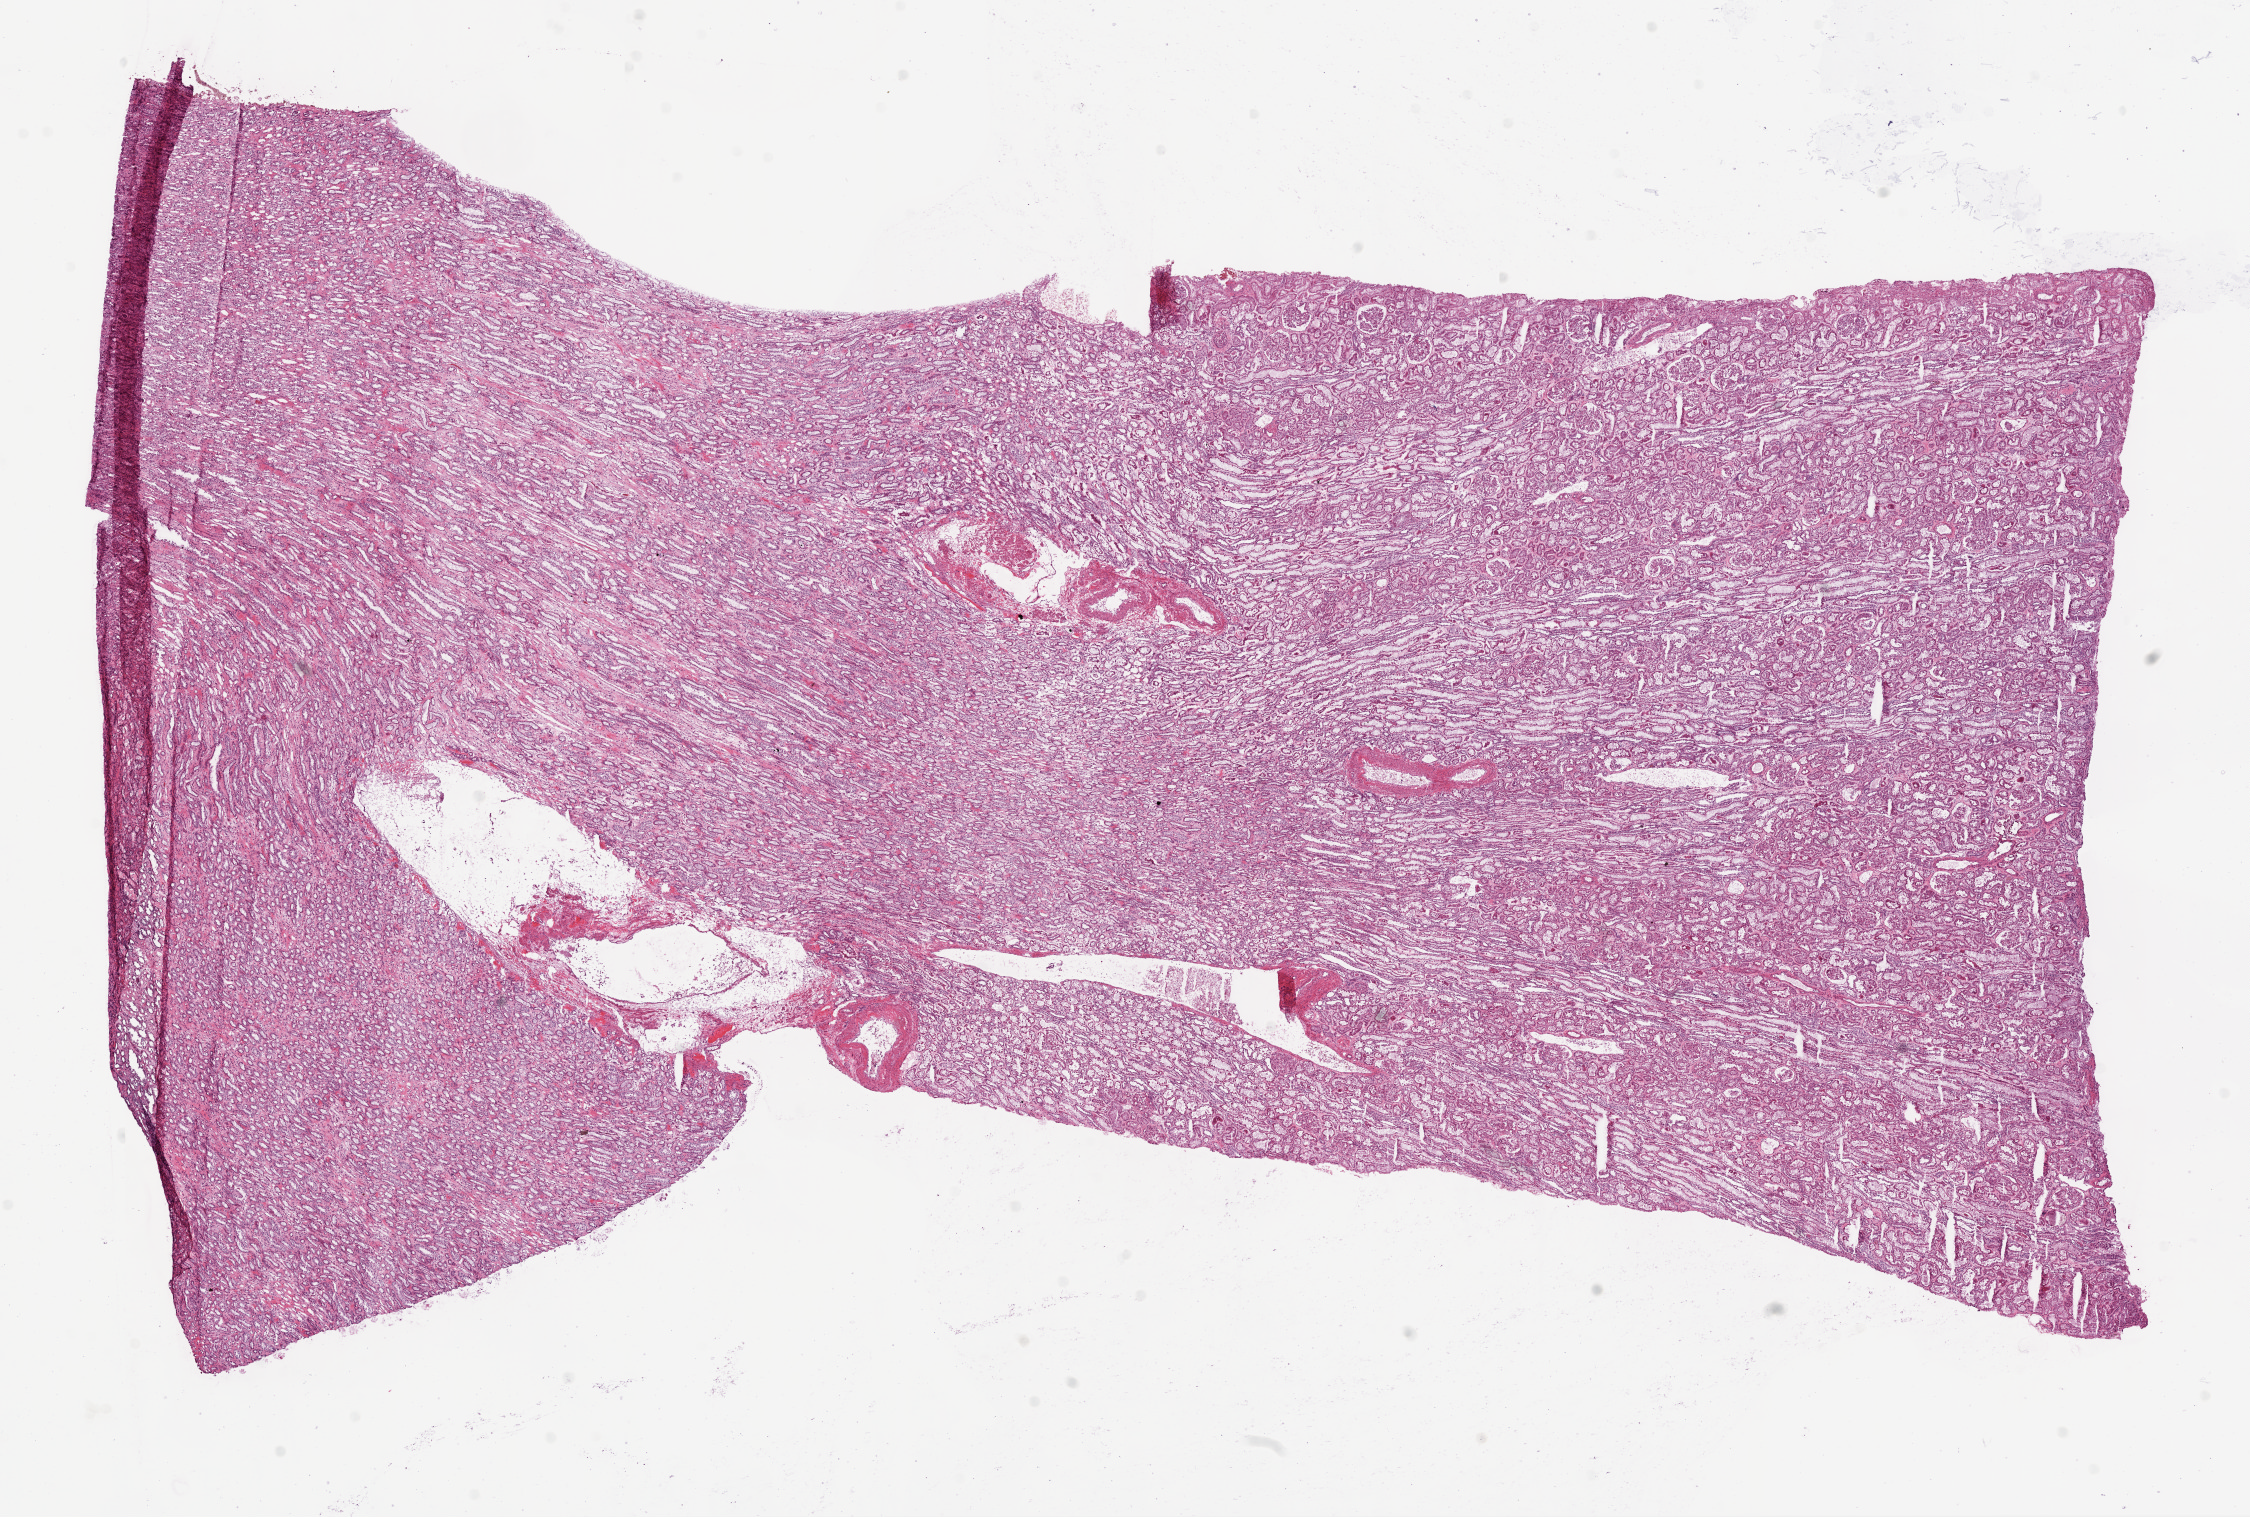
Digitized H&E tissue section (whole slide) — shown as a low-resolution overview of the whole scanned area (about 18.1 x 12.2 mm), frozen section, sample: solid tissue normal (non-tumour tissue), kidney. Male, age 49 years at initial diagnosis.
• this section: solid tissue normal sample (biorepository sample class)
• patient diagnosis: Clear cell adenocarcinoma, NOS